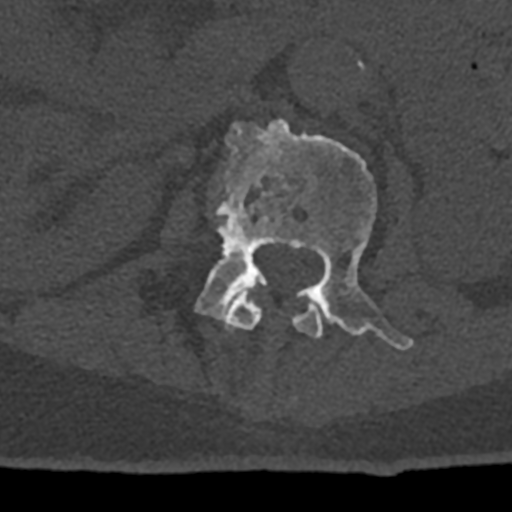
CT including the spine, one axial slice; reconstruction kernel Br40s/3; bone window (W 1800 / L 400 HU); 512 × 512 image matrix, field of view 160 × 160 mm. Patient: male, 74 years. From the clinical record (not read from this slice): primary cancer: renal; vertebrae with lytic lesions (as recorded): T10, L1, L2, L3, L4, L5.
Annotated regions visible in this slice (semi-automatic segmentation, software-assisted and operator-edited):
- L1 vertebra: bounding box <225,287,323,338> (left, top, right, bottom; pixels)
- L2 vertebra: <195,118,413,350>